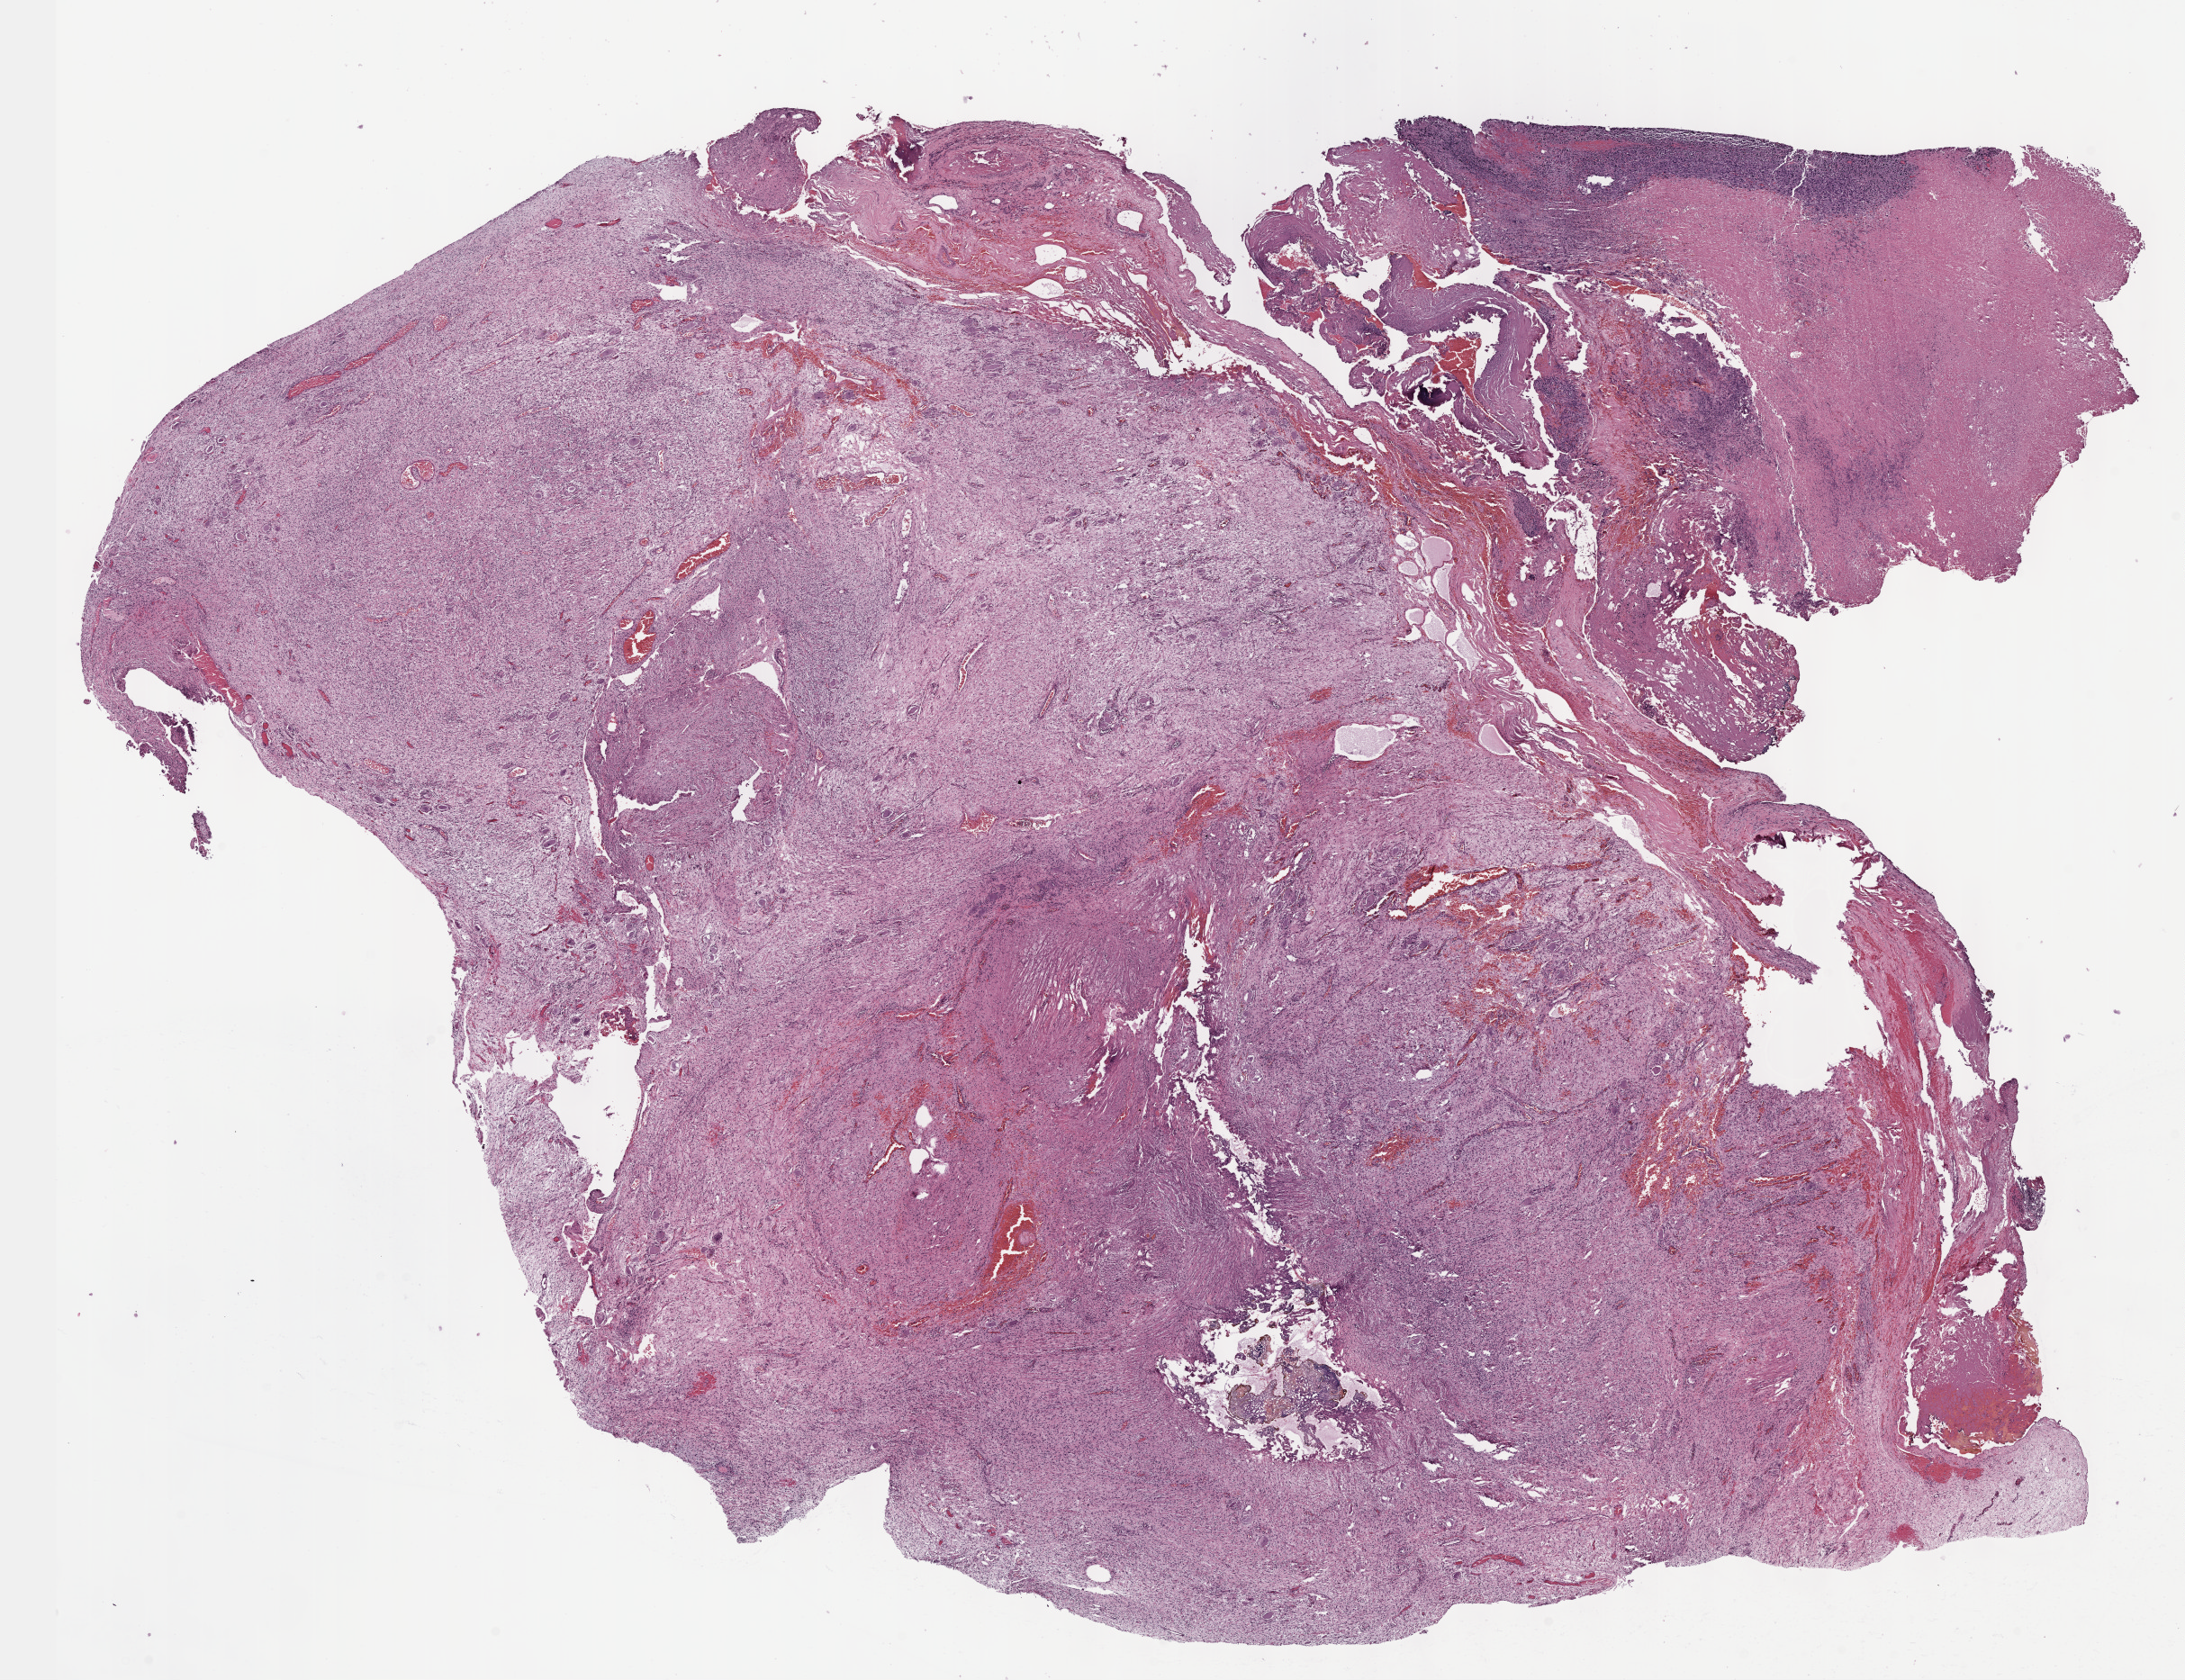
Whole-slide histology image, H&E — low-resolution overview of the scanned area, about 19.6 x 15.1 mm, FFPE section, primary tumour sample from the peripheral nerves and autonomic nervous system. Male patient; age at initial diagnosis 50 years.
Pathologic diagnosis: Malignant peripheral nerve sheath tumor.